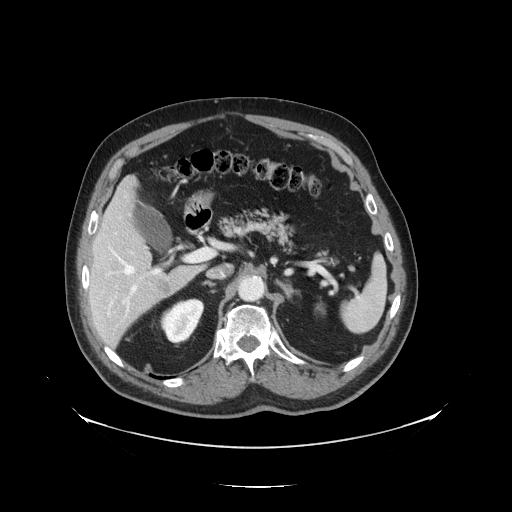
Contrast-enhanced abdominal CT, one axial slice. Position 81 of 138 along the scan axis. Reconstruction kernel STANDARD. Intravenous contrast given. Soft-tissue window (W 400 / L 40 HU). 2.5 mm slice thickness. 512 × 512 image matrix. Male patient, age 77 years. From the clinical record (not read from this slice): diagnosis: colorectal cancer liver metastases, imaged before liver resection; multiple liver metastases: no; largest metastasis: 1.5 cm; disease in both lobes: no.
Outlined on this slice (manually delineated by an expert):
- hepatic veins: bounding box [x1, y1, x2, y2] px = [111, 250, 135, 275]
- liver: [89, 180, 201, 346]
- planned liver remnant (the part of the liver to remain after resection): [89, 180, 155, 288]
- portal vein (with intrahepatic branches): [122, 252, 205, 316]
- liver metastasis: [158, 280, 172, 295]